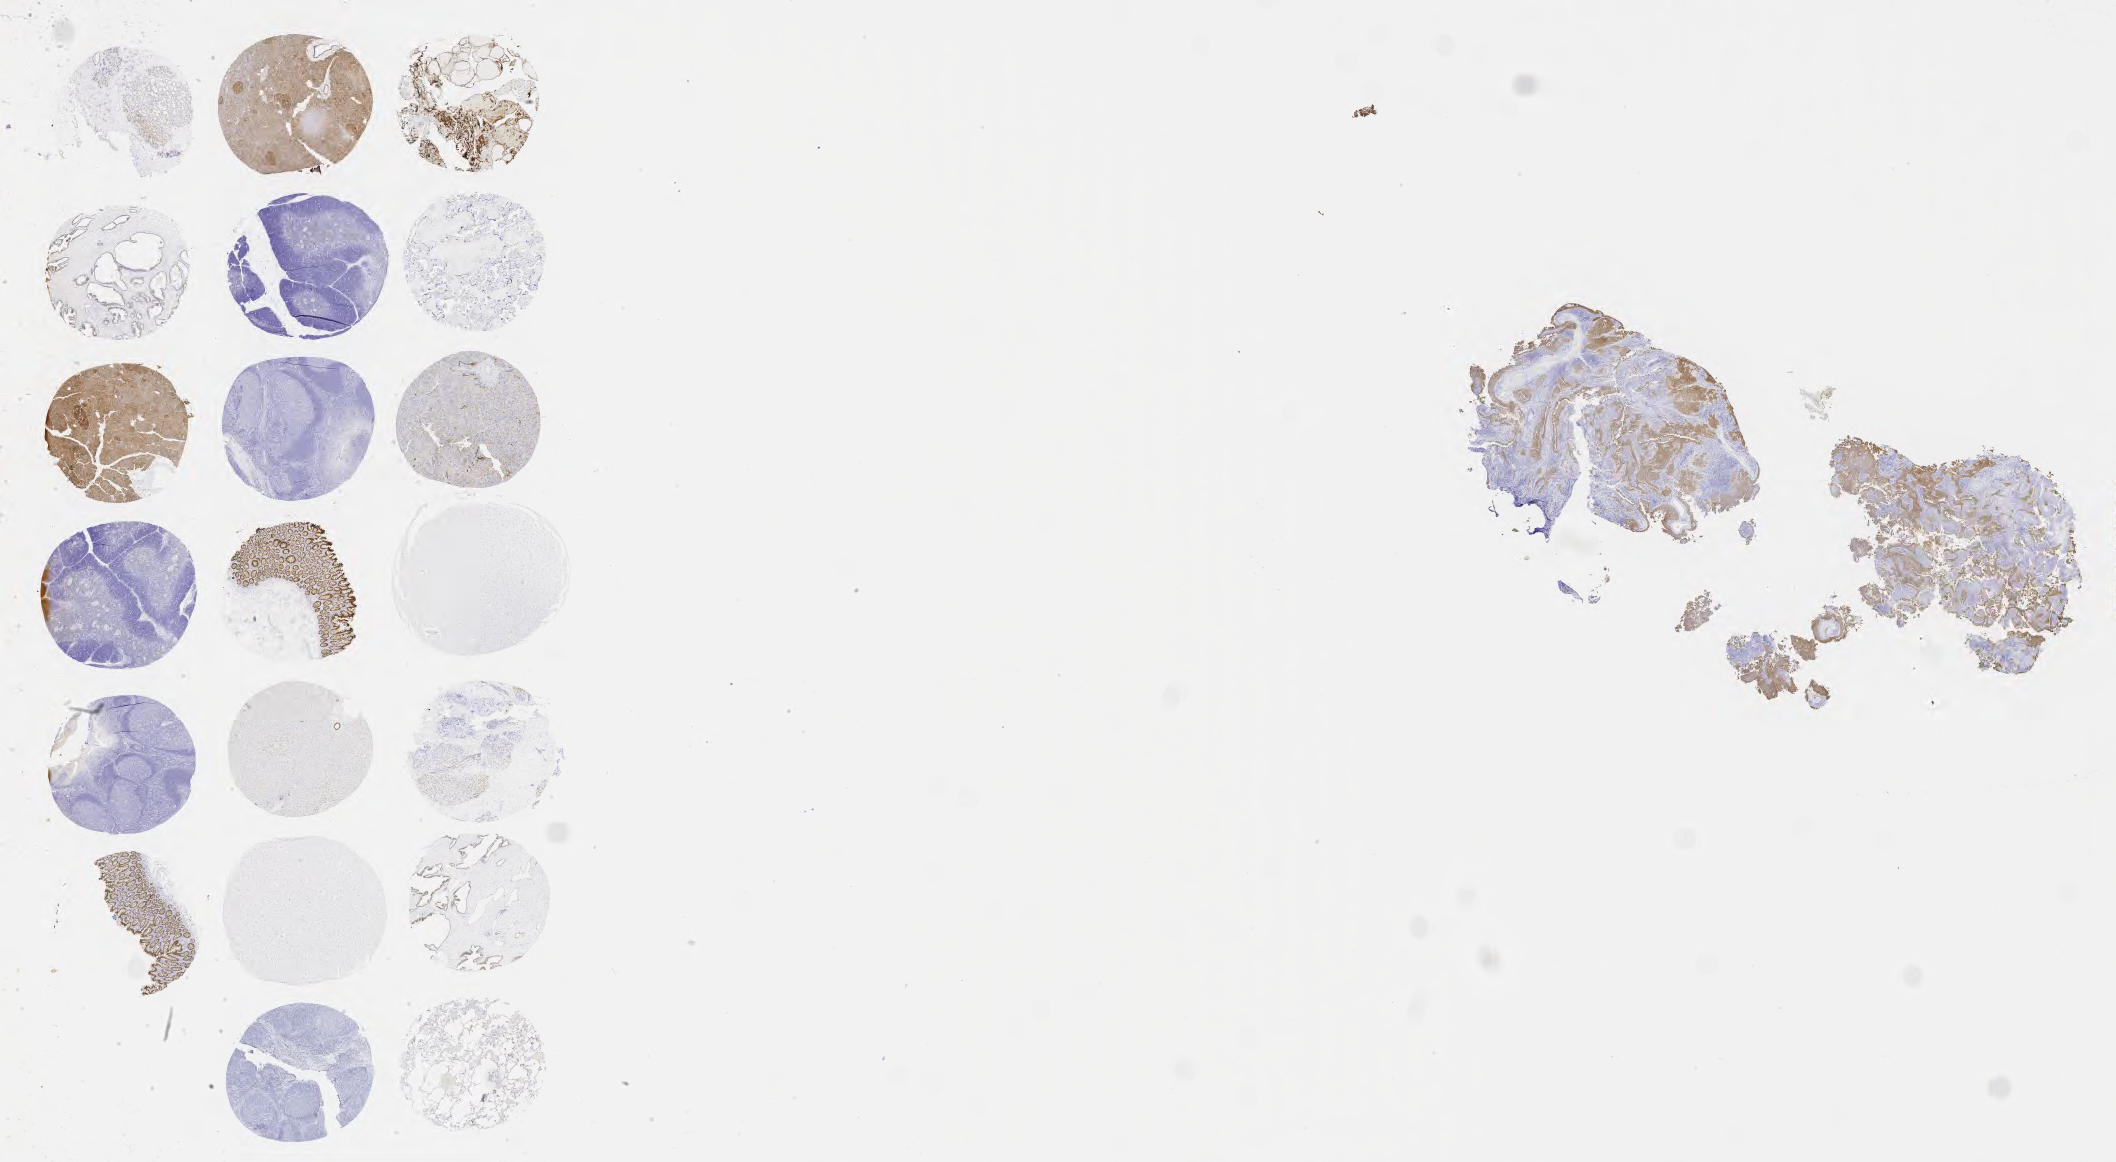
IHC for MOC-31 (anti-EpCAM), whole-slide image, shown as a low-resolution overview of the whole scanned area (about 34.2 x 18.8 mm). Specimen: tumor tissue. Site: cervix. Patient: female, age 65 years.
Diagnosis: Squamous cell carcinoma, large cell, nonkeratinizing, NOS.